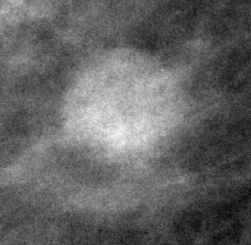
Cropped region of a digitized screen-film mammogram centred on a radiologist-marked abnormality; right breast; MLO view; BI-RADS breast density category 2 (scale 1–4).
Finding: mass, shape round, margins circumscribed; BI-RADS assessment category 4; subtlety rating 5 on a 1 (subtle) to 5 (obvious) scale; pathology (as recorded): malignant.